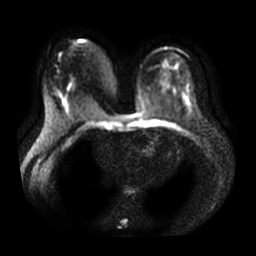
Breast MRI, one axial slice. Position 20 of 35 along the scan axis. Diffusion-weighted series; image 2 of 4 stored at this slice position (different b-values; order by instance number). 3 T. 5 mm slice thickness. 256 × 256 image matrix, field of view 360 × 360 mm. Female patient.
Annotated regions visible in this slice (outlined manually by an expert reader):
- tumour on diffusion-weighted imaging: box from (x=63, y=98) to (x=67, y=107) px